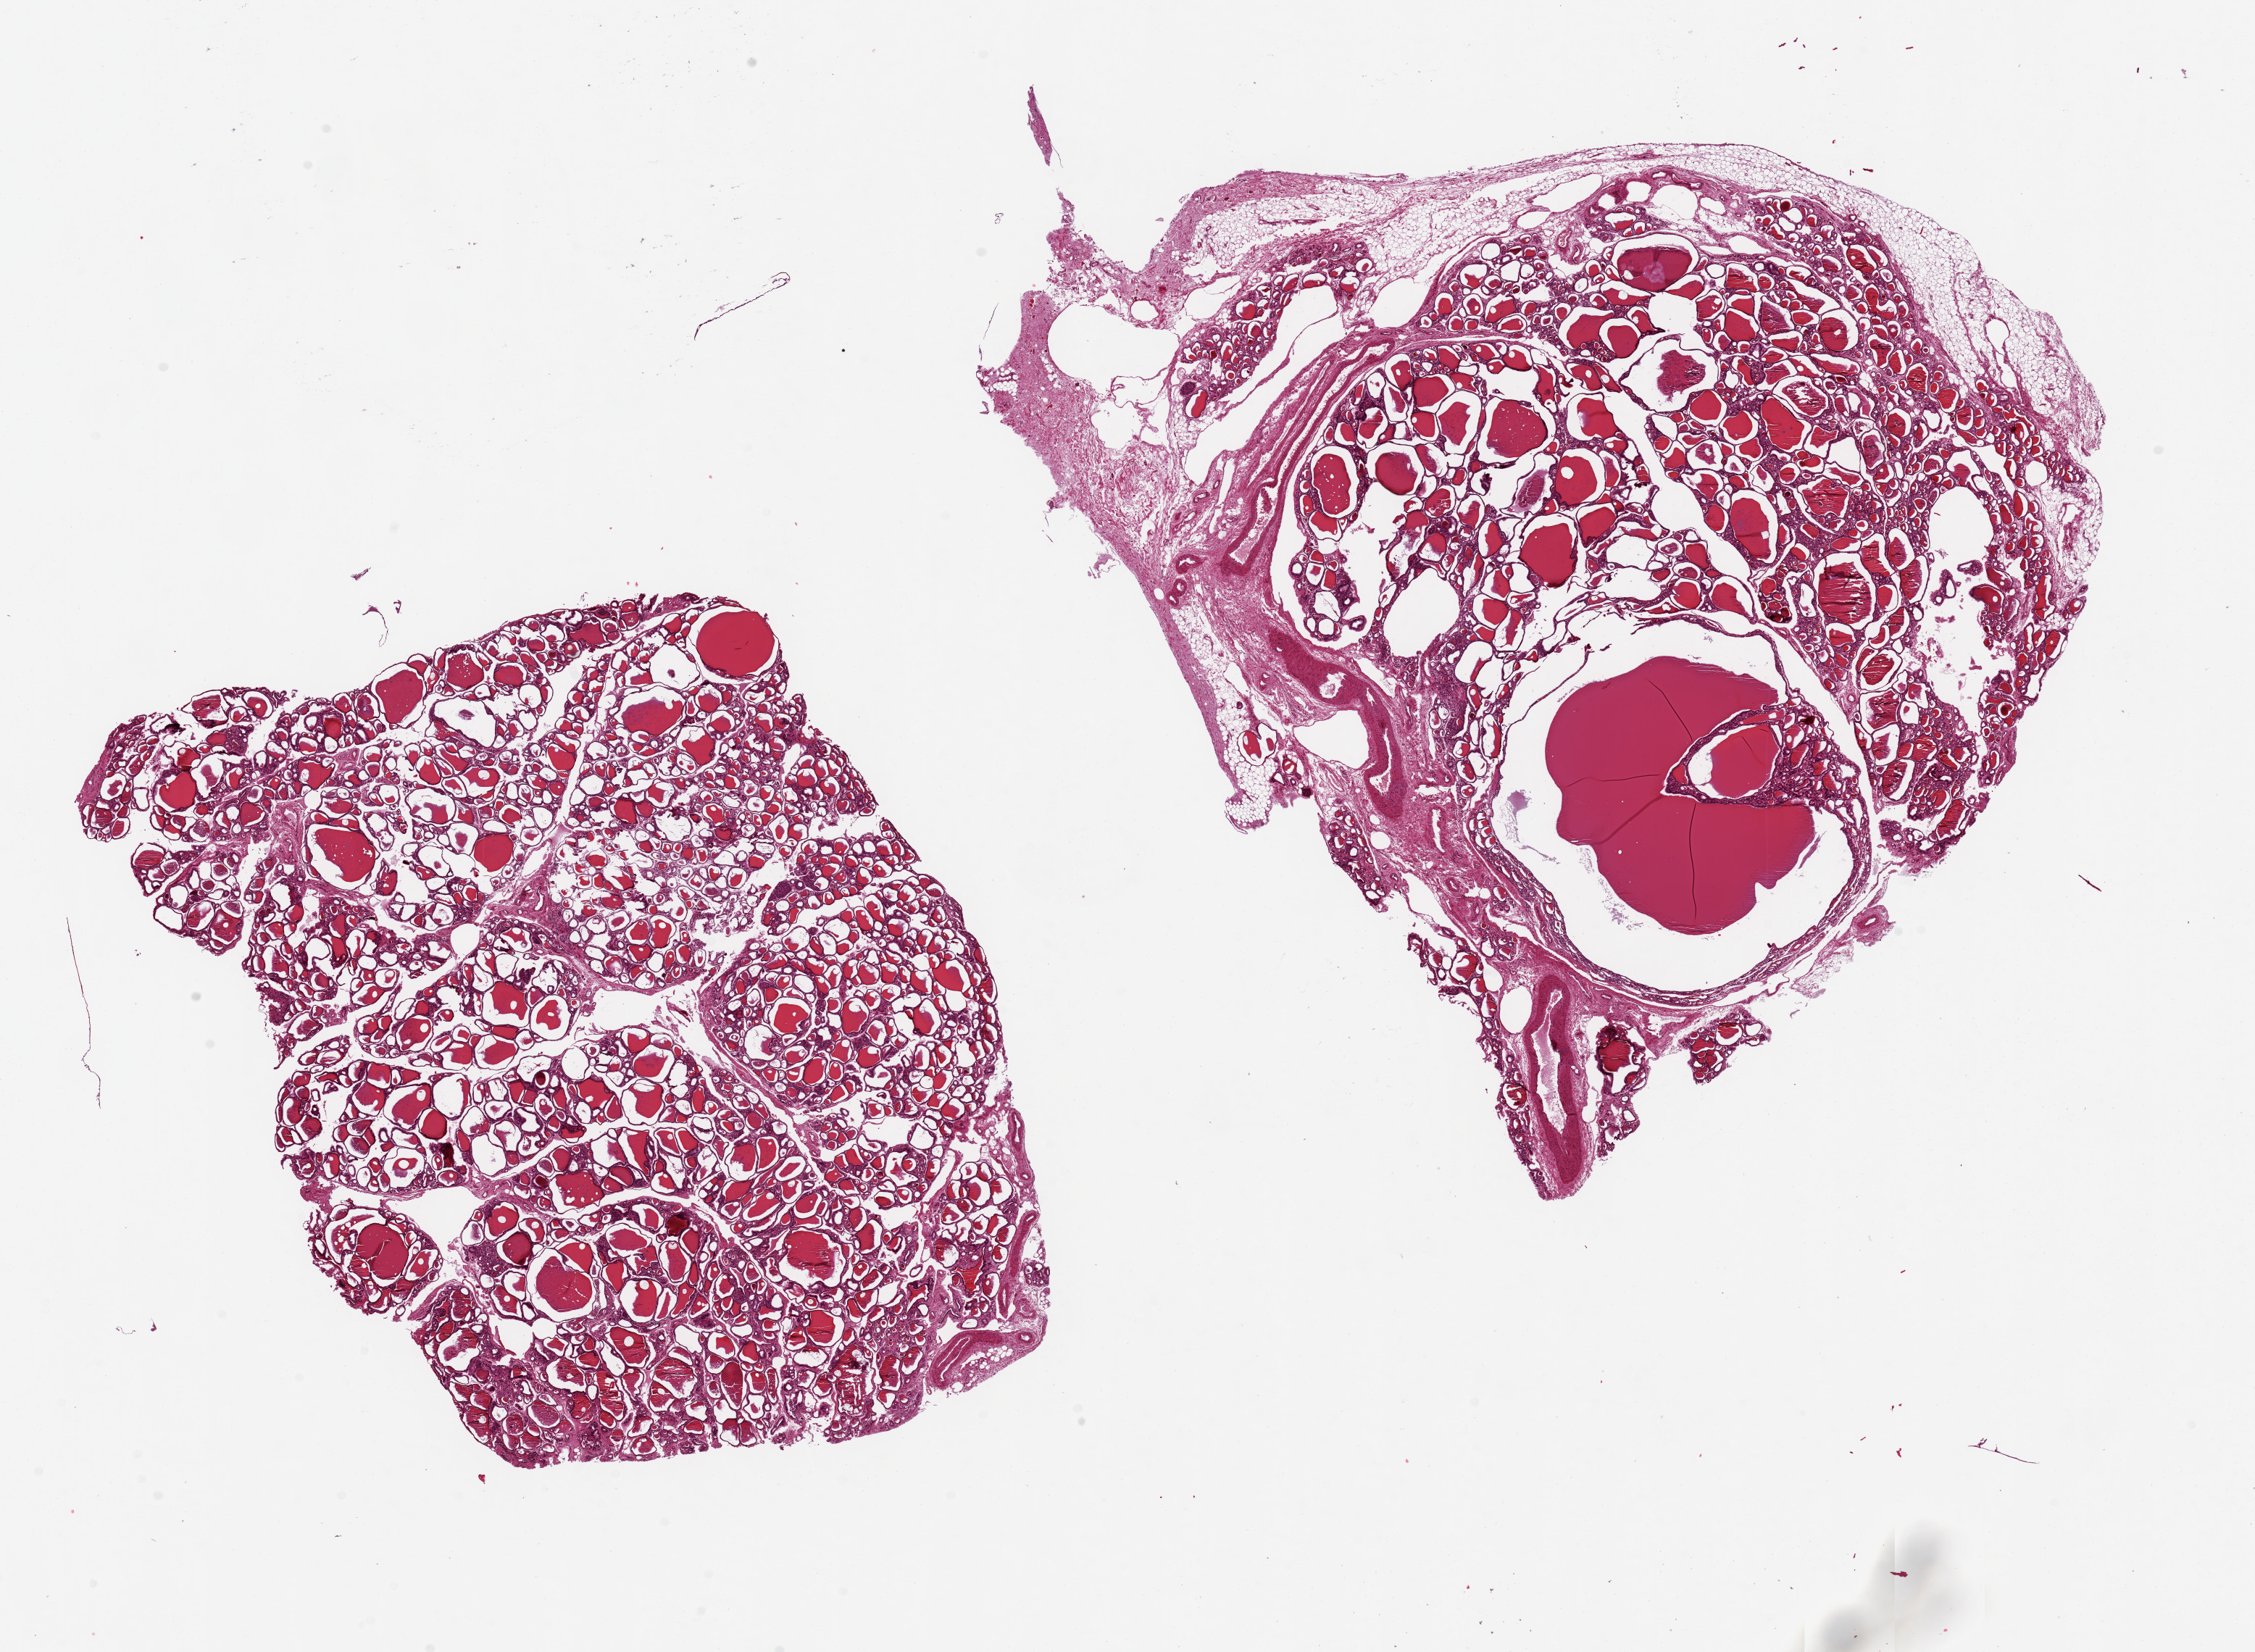
Whole-slide image, haematoxylin and eosin stain — shown as a low-resolution overview of the whole scanned area (about 24.6 x 18.0 mm), PAXgene-fixed paraffin-embedded (PFPE) section, target tissue: thyroid, tissue donor sample.
Review note (as recorded): 2 pieces 11x9 & 9x4 mm; 1, 4mm cystic follicle.